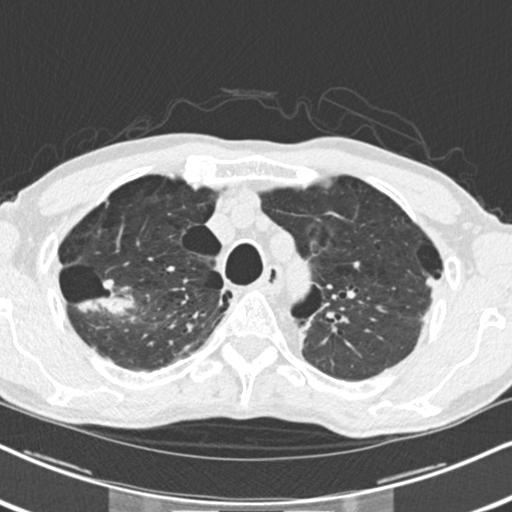
Low-dose screening chest CT, axial slice. Baseline screening round. Lung window (W 1500 / L -600 HU). 2 mm slice thickness. Standard (soft-tissue) reconstruction kernel (B30f). Male, age 71 years at enrolment.
- Lesion marked by an expert reader, bounding box [x1, y1, x2, y2] px = [89, 266, 146, 316].
- The screening reader recorded 2 non-calcified nodules or masses ≥4 mm on this exam (right upper lobe, left upper lobe); which of them this box marks is not recorded.
- Official screen result: positive, change unspecified: nodule(s) >= 4 mm or enlarging nodule(s), mass(es), or other non-specific abnormalities suspicious for lung cancer.